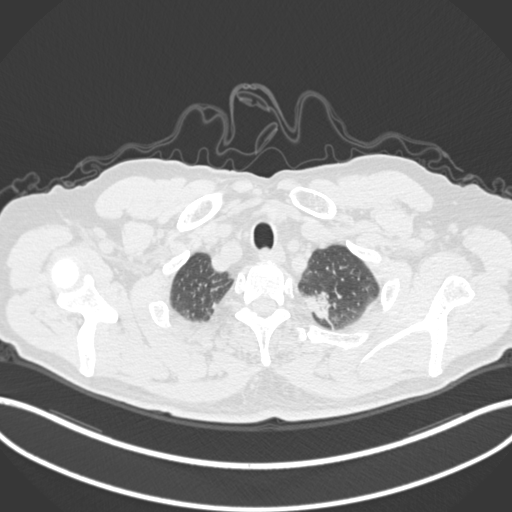
Chest CT, one axial slice. Slice 291 of 306 in the series (ordered by position). Reconstruction kernel B30f. 120 kVp. Lung window (W 1500 / L -600 HU). 512 × 512 image matrix, field of view 400 × 400 mm. Patient: male, 64 years. From the clinical record (not read from this slice): clinical TNM (as recorded): T1c N0 M0.
Annotated regions visible in this slice (bounding box drawn by a radiologist):
- lung tumour (recorded histology: adenocarcinoma): box from (x=305, y=292) to (x=334, y=324) px